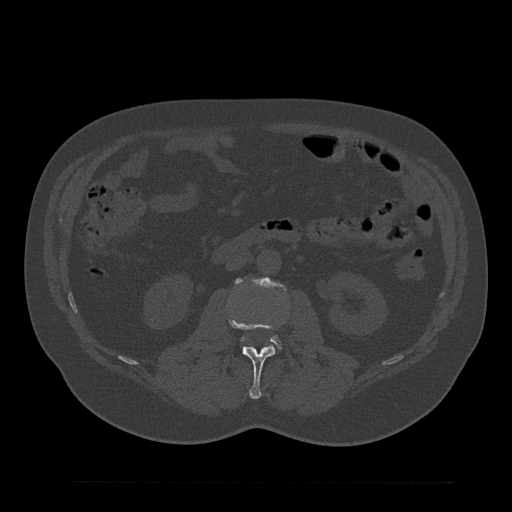
CT including the spine, one axial slice. Slice 76 of 797 in the series (ordered by position). 120 kVp. Bone window (W 1800 / L 400 HU). 0.5 mm slice thickness. 512 × 512 image matrix, field of view 430 × 430 mm. Male patient, age 61 years. From the clinical record (not read from this slice): primary cancer: prostate.
Annotated regions visible in this slice (semi-automatic segmentation, software-assisted and operator-edited):
- L2 vertebra: bounding box [x1, y1, x2, y2] px = [228, 317, 276, 399]
- L3 vertebra: [237, 279, 281, 348]